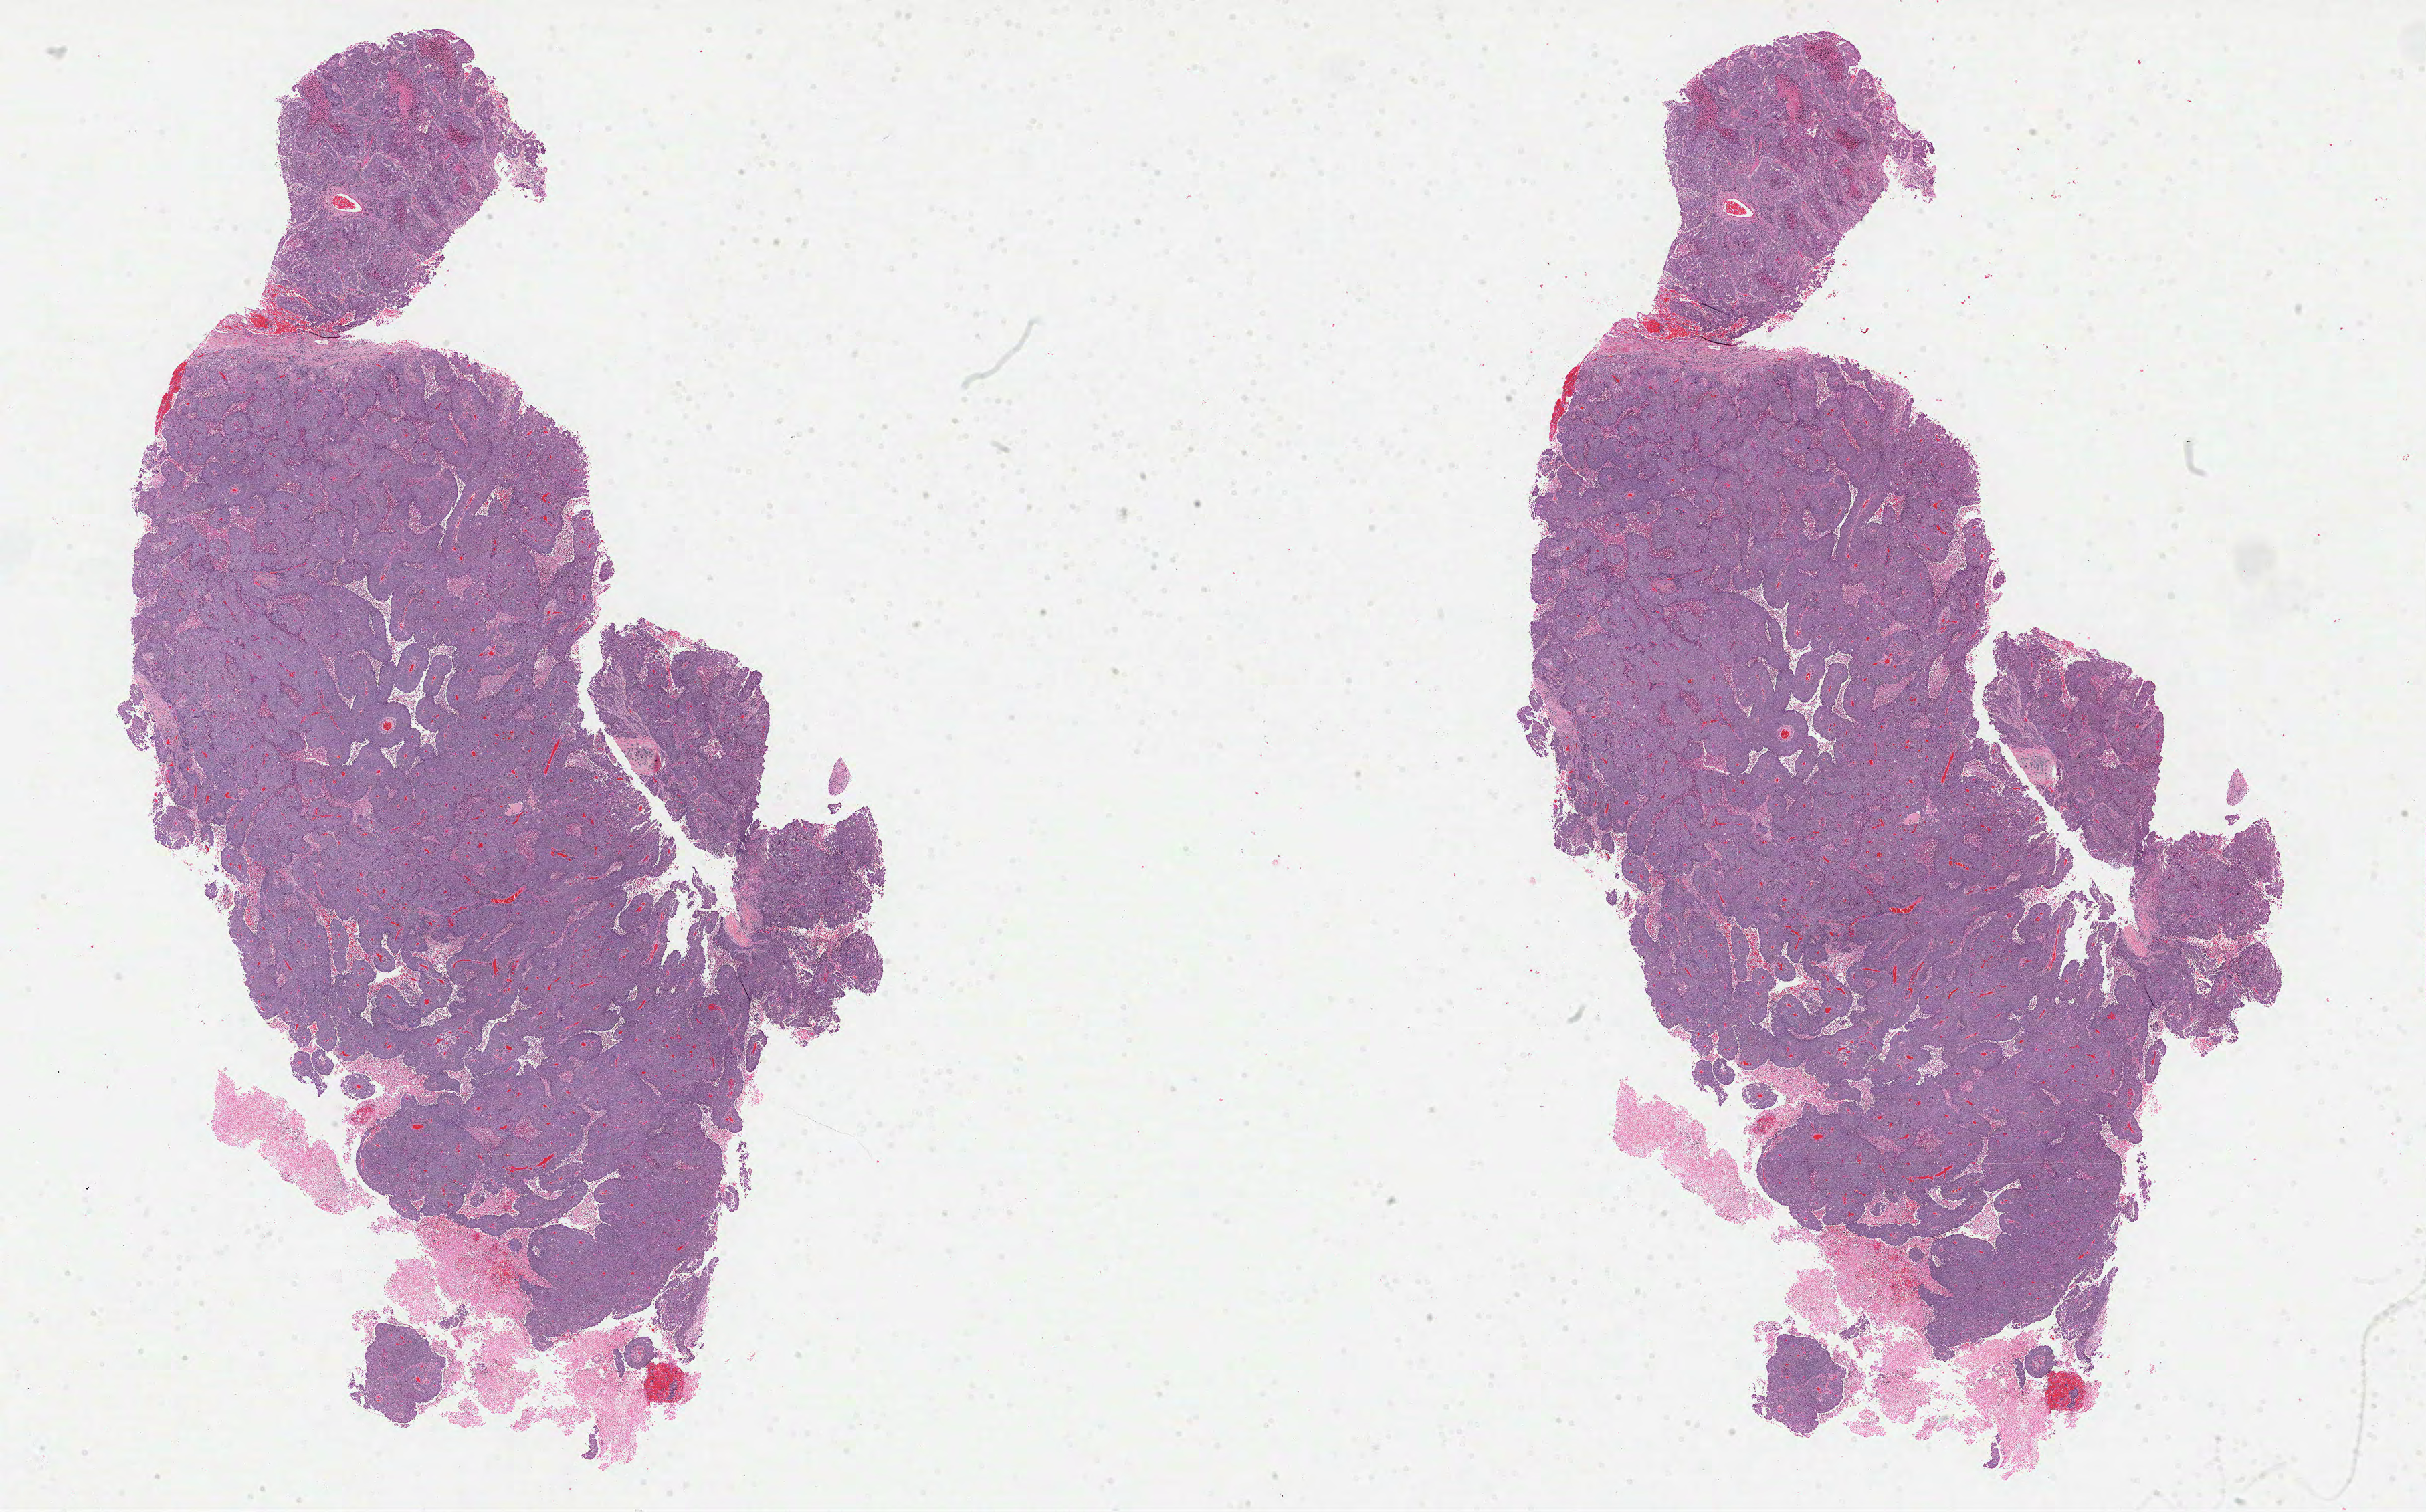
H&E-stained whole-slide image — a low-resolution overview of the entire scanned area, about 29.2 x 18.2 mm; FFPE section; lung, primary tumour sample. Patient: female, age at initial diagnosis 75 years.
Histologic diagnosis: Papillary adenocarcinoma, NOS (upper lobe, lung).